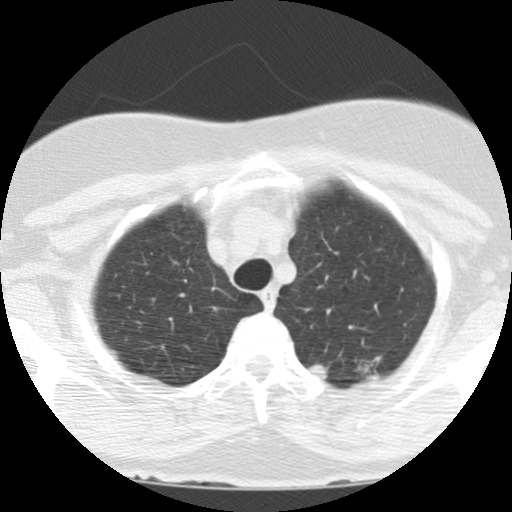
Axial slice from a low-dose chest CT screening exam, baseline annual screen, lung window (W 1500 / L -600 HU), 2.5 mm slice thickness, slice 18 of 123 in the series. Female participant, aged 60 years at enrolment. Former smoker at enrolment.
Expert-annotated lung lesion, bounding box <300,357,337,385> (left, top, right, bottom; pixels). The screening reader recorded 3 non-calcified nodules or masses ≥4 mm on this exam; which of them this box marks is not recorded. Later outcome: lung cancer diagnosed 31 days after this screen — bronchiolo-alveolar adenocarcinoma, NOS, left upper lobe, moderately differentiated (G2), stage IA (AJCC 6th edition), 15 mm at pathology.